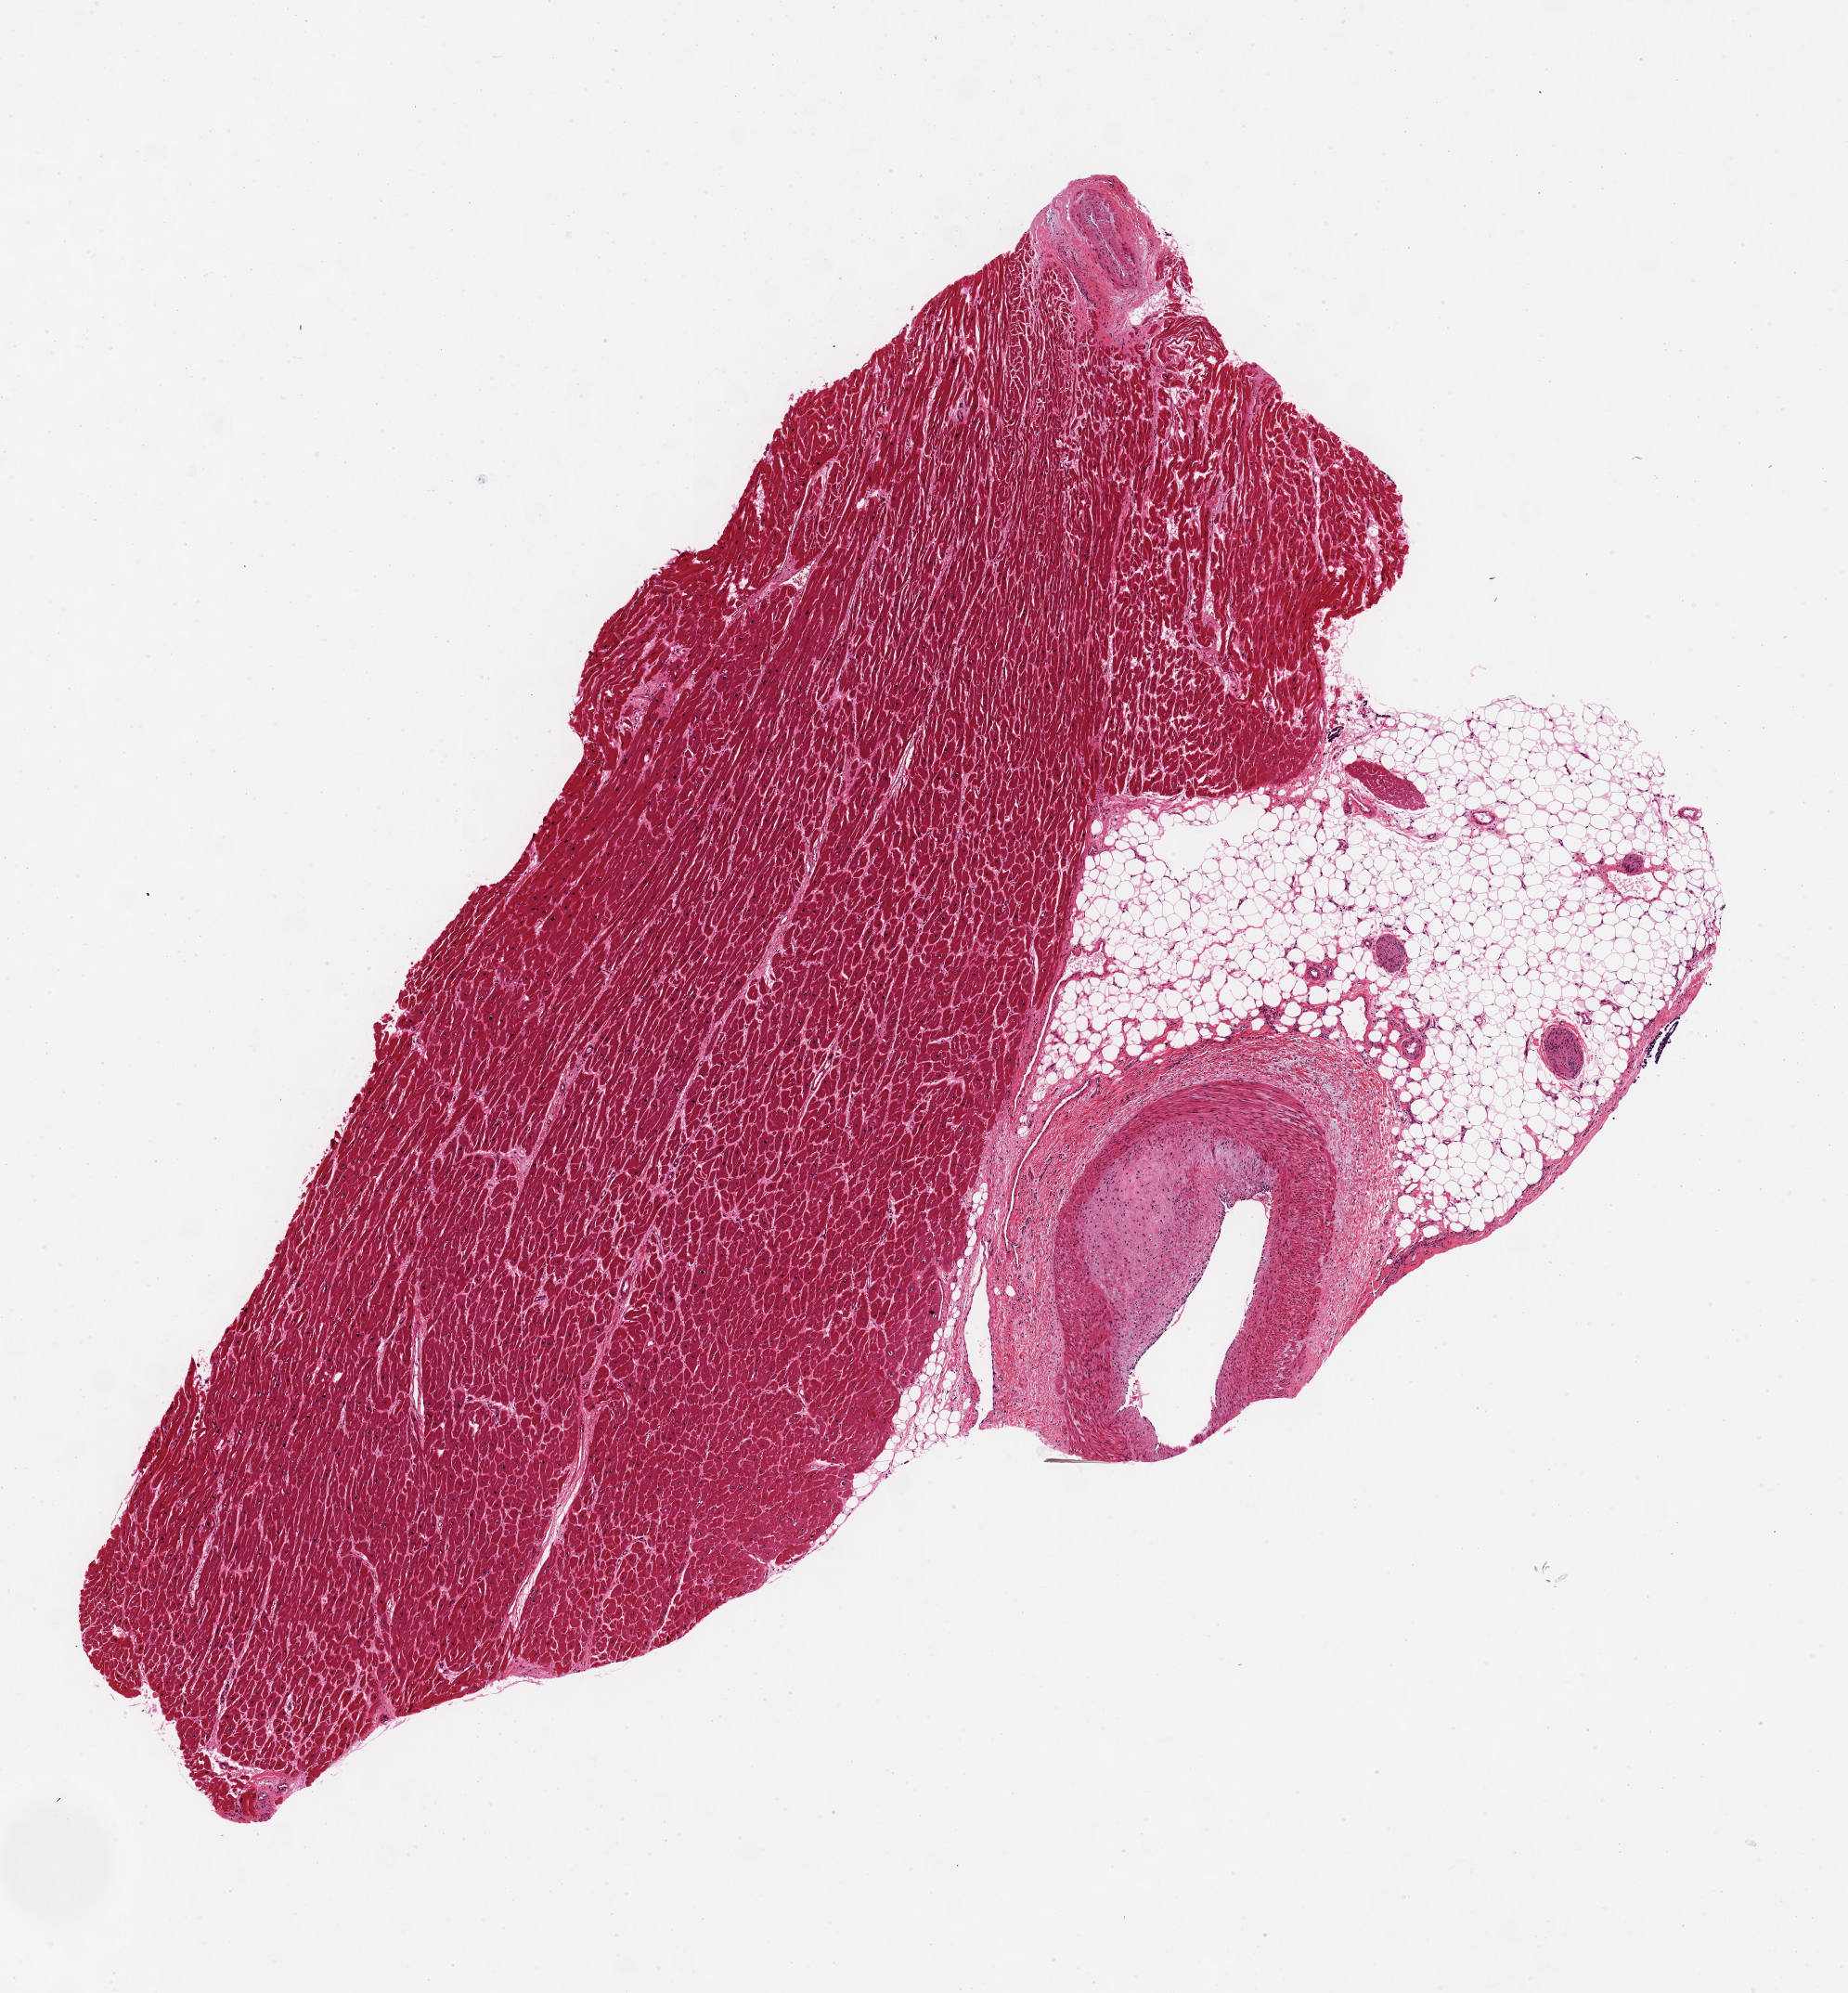
Digitized haematoxylin and eosin-stained section, whole scanned area (about 7.9 x 8.5 mm) shown as a low-resolution overview, PAXgene-fixed paraffin-embedded (PFPE) section, sampled site (target tissue): coronary artery, donor tissue sample. Donor sex: male.
Review note (as recorded): Artery is about 10% of tissue area; rest is fat and myocardium. Artery has ~ 50% atherosclerotic occlusion.